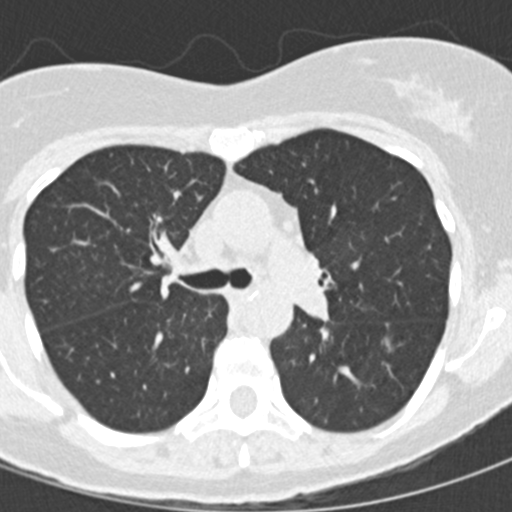
Low-dose screening chest CT, one axial slice. Slice 94 of 145 in the series (ordered by position). Lung window (W 1500 / L -600 HU). 2 mm slice thickness. 512 × 512 image matrix, field of view 270 × 270 mm.
Annotated regions visible in this slice (outlined manually by an expert reader):
- lesion 1 (tumor, lower lobe of left lung): box from (x=382, y=337) to (x=394, y=353) px